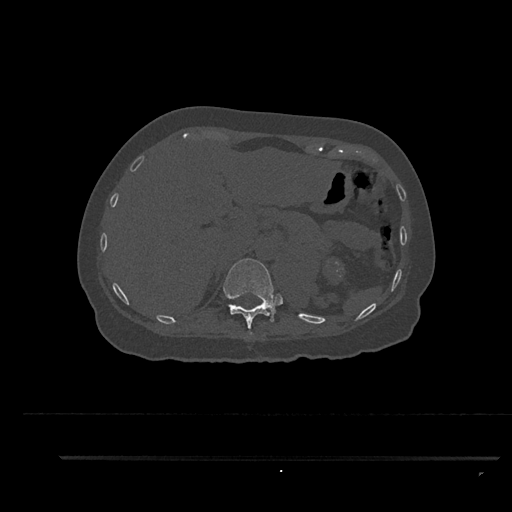
CT including the spine, one axial slice. Position 313 of 797 along the scan axis. Reconstruction kernel Br40s/3. 120 kVp. Bone window (W 1800 / L 400 HU). 0.5 mm slice thickness. 512 × 512 image matrix. Patient: female, 44 years. Case-level facts recorded for this patient, not image findings: primary cancer: renal.
Annotated regions visible in this slice (semi-automatic segmentation, software-assisted and operator-edited):
- T11 vertebra: bounding box [x1, y1, x2, y2] px = [223, 258, 276, 339]